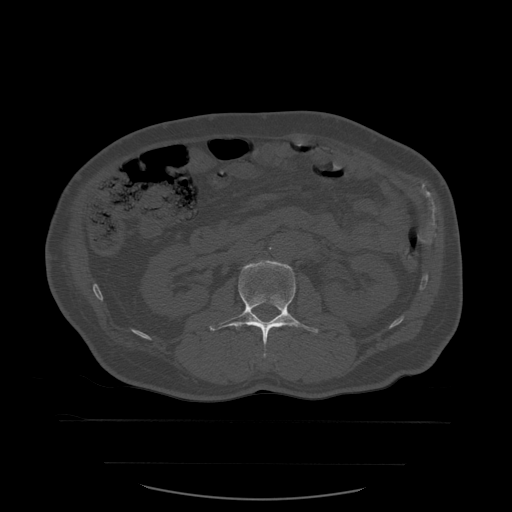
CT including the spine, one axial slice. Position 219 of 590 along the scan axis. Bone window (W 1800 / L 400 HU). 512 × 512 image matrix, field of view 479 × 479 mm. Patient age 71 years. Case-level facts recorded for this patient, not image findings: primary cancer: lung; vertebrae with lytic lesions (as recorded): T1, T2, L5, S1.
Structures marked on this image (semi-automatically segmented with operator editing):
- L2 vertebra: box from (x=210, y=260) to (x=320, y=357) px